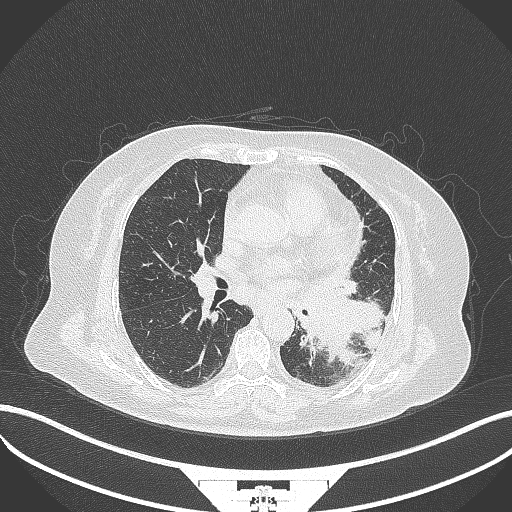
Chest CT, one axial slice. Reconstruction kernel B70f. Lung window (W 1500 / L -600 HU). 512 × 512 image matrix, field of view 400 × 400 mm. Patient: female, 69 years. From the clinical record (not read from this slice): clinical TNM (as recorded): T2b N3 M1.
Annotated regions visible in this slice (bounding box drawn by a radiologist):
- lung tumour (recorded histology: adenocarcinoma): box from (x=300, y=289) to (x=387, y=366) px